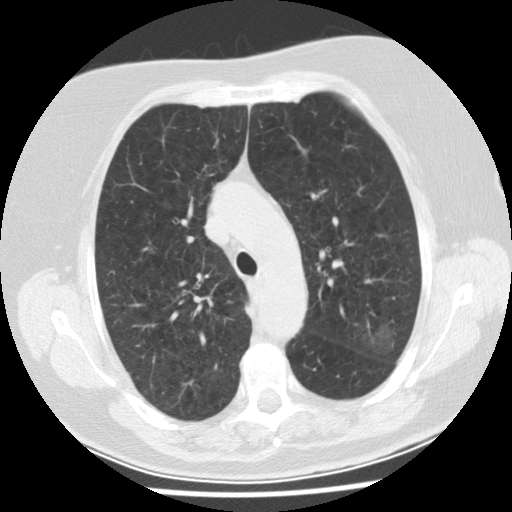
Chest CT (low-dose screening protocol), one axial image. Baseline screening round. Lung window (W 1500 / L -600 HU). Standard (soft-tissue) reconstruction kernel (STANDARD). Female participant, aged 74 years at enrolment.
Expert-annotated lung lesion, bounding box (x1, y1, x2, y2) in pixels: (336, 310, 408, 367). The screening reader recorded 2 non-calcified nodules or masses ≥4 mm on this exam; which of them this box marks is not recorded. Lung cancer was diagnosed 532 days after this screen: bronchiolo-alveolar adenocarcinoma, NOS, left upper lobe, stage IA (AJCC 6th edition), 20 mm at pathology.